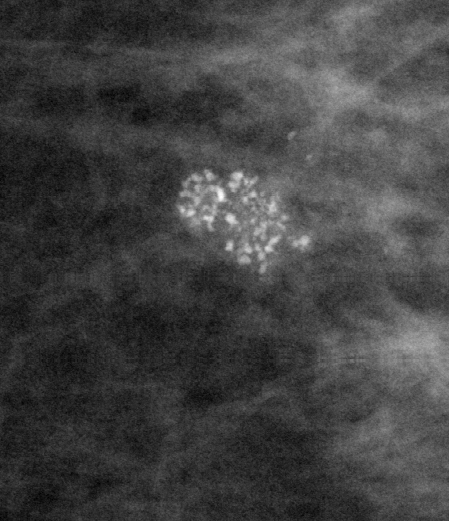
Crop from a digitized film mammogram around one marked abnormality, left breast, CC view, BI-RADS breast density category 2 (scale 1–4).
Marked abnormality: calcifications, morphology pleomorphic, distribution clustered; BI-RADS assessment category 5; subtlety rating 5 on a 1 (subtle) to 5 (obvious) scale; pathology result (as recorded, not read from the image): malignant.